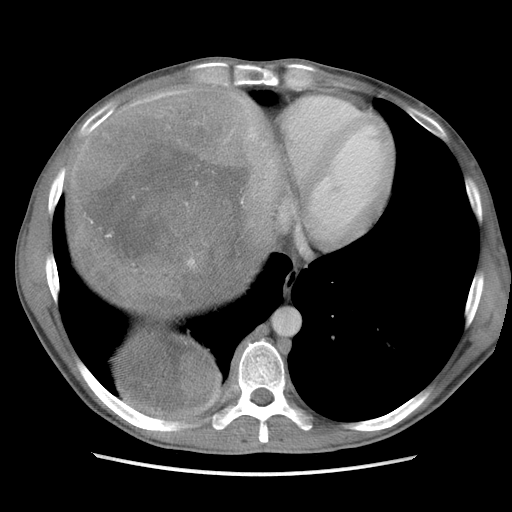
Contrast-enhanced abdominal CT, one axial slice; position 94 of 115 along the scan axis; soft-tissue window (W 400 / L 40 HU); 512 × 512 image matrix, field of view 360 × 360 mm. Male patient. From the clinical record (not read from this slice): diagnosis: adrenocortical carcinoma; tumour side: right adrenal; Ki-67 index: 13 %; stage (as recorded): 3.
Annotated regions visible in this slice (semi-automatic segmentation, software-assisted and operator-edited):
- mass: bounding box (x1, y1, x2, y2) in pixels: (70, 90, 291, 416)